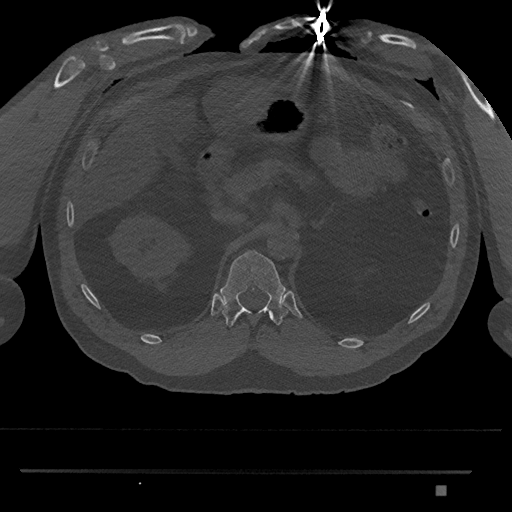
CT including the spine, one axial slice. Slice 896 of 1134 in the series (ordered by position). Reconstruction kernel Br40s/3. 120 kVp. Bone window (W 1800 / L 400 HU). 512 × 512 image matrix, field of view 429 × 429 mm. Male patient, age 65 years. From the clinical record (not read from this slice): primary cancer: prostate.
Structures marked on this image (semi-automatically segmented with operator editing):
- T12 vertebra: box from (x=220, y=250) to (x=289, y=328) px